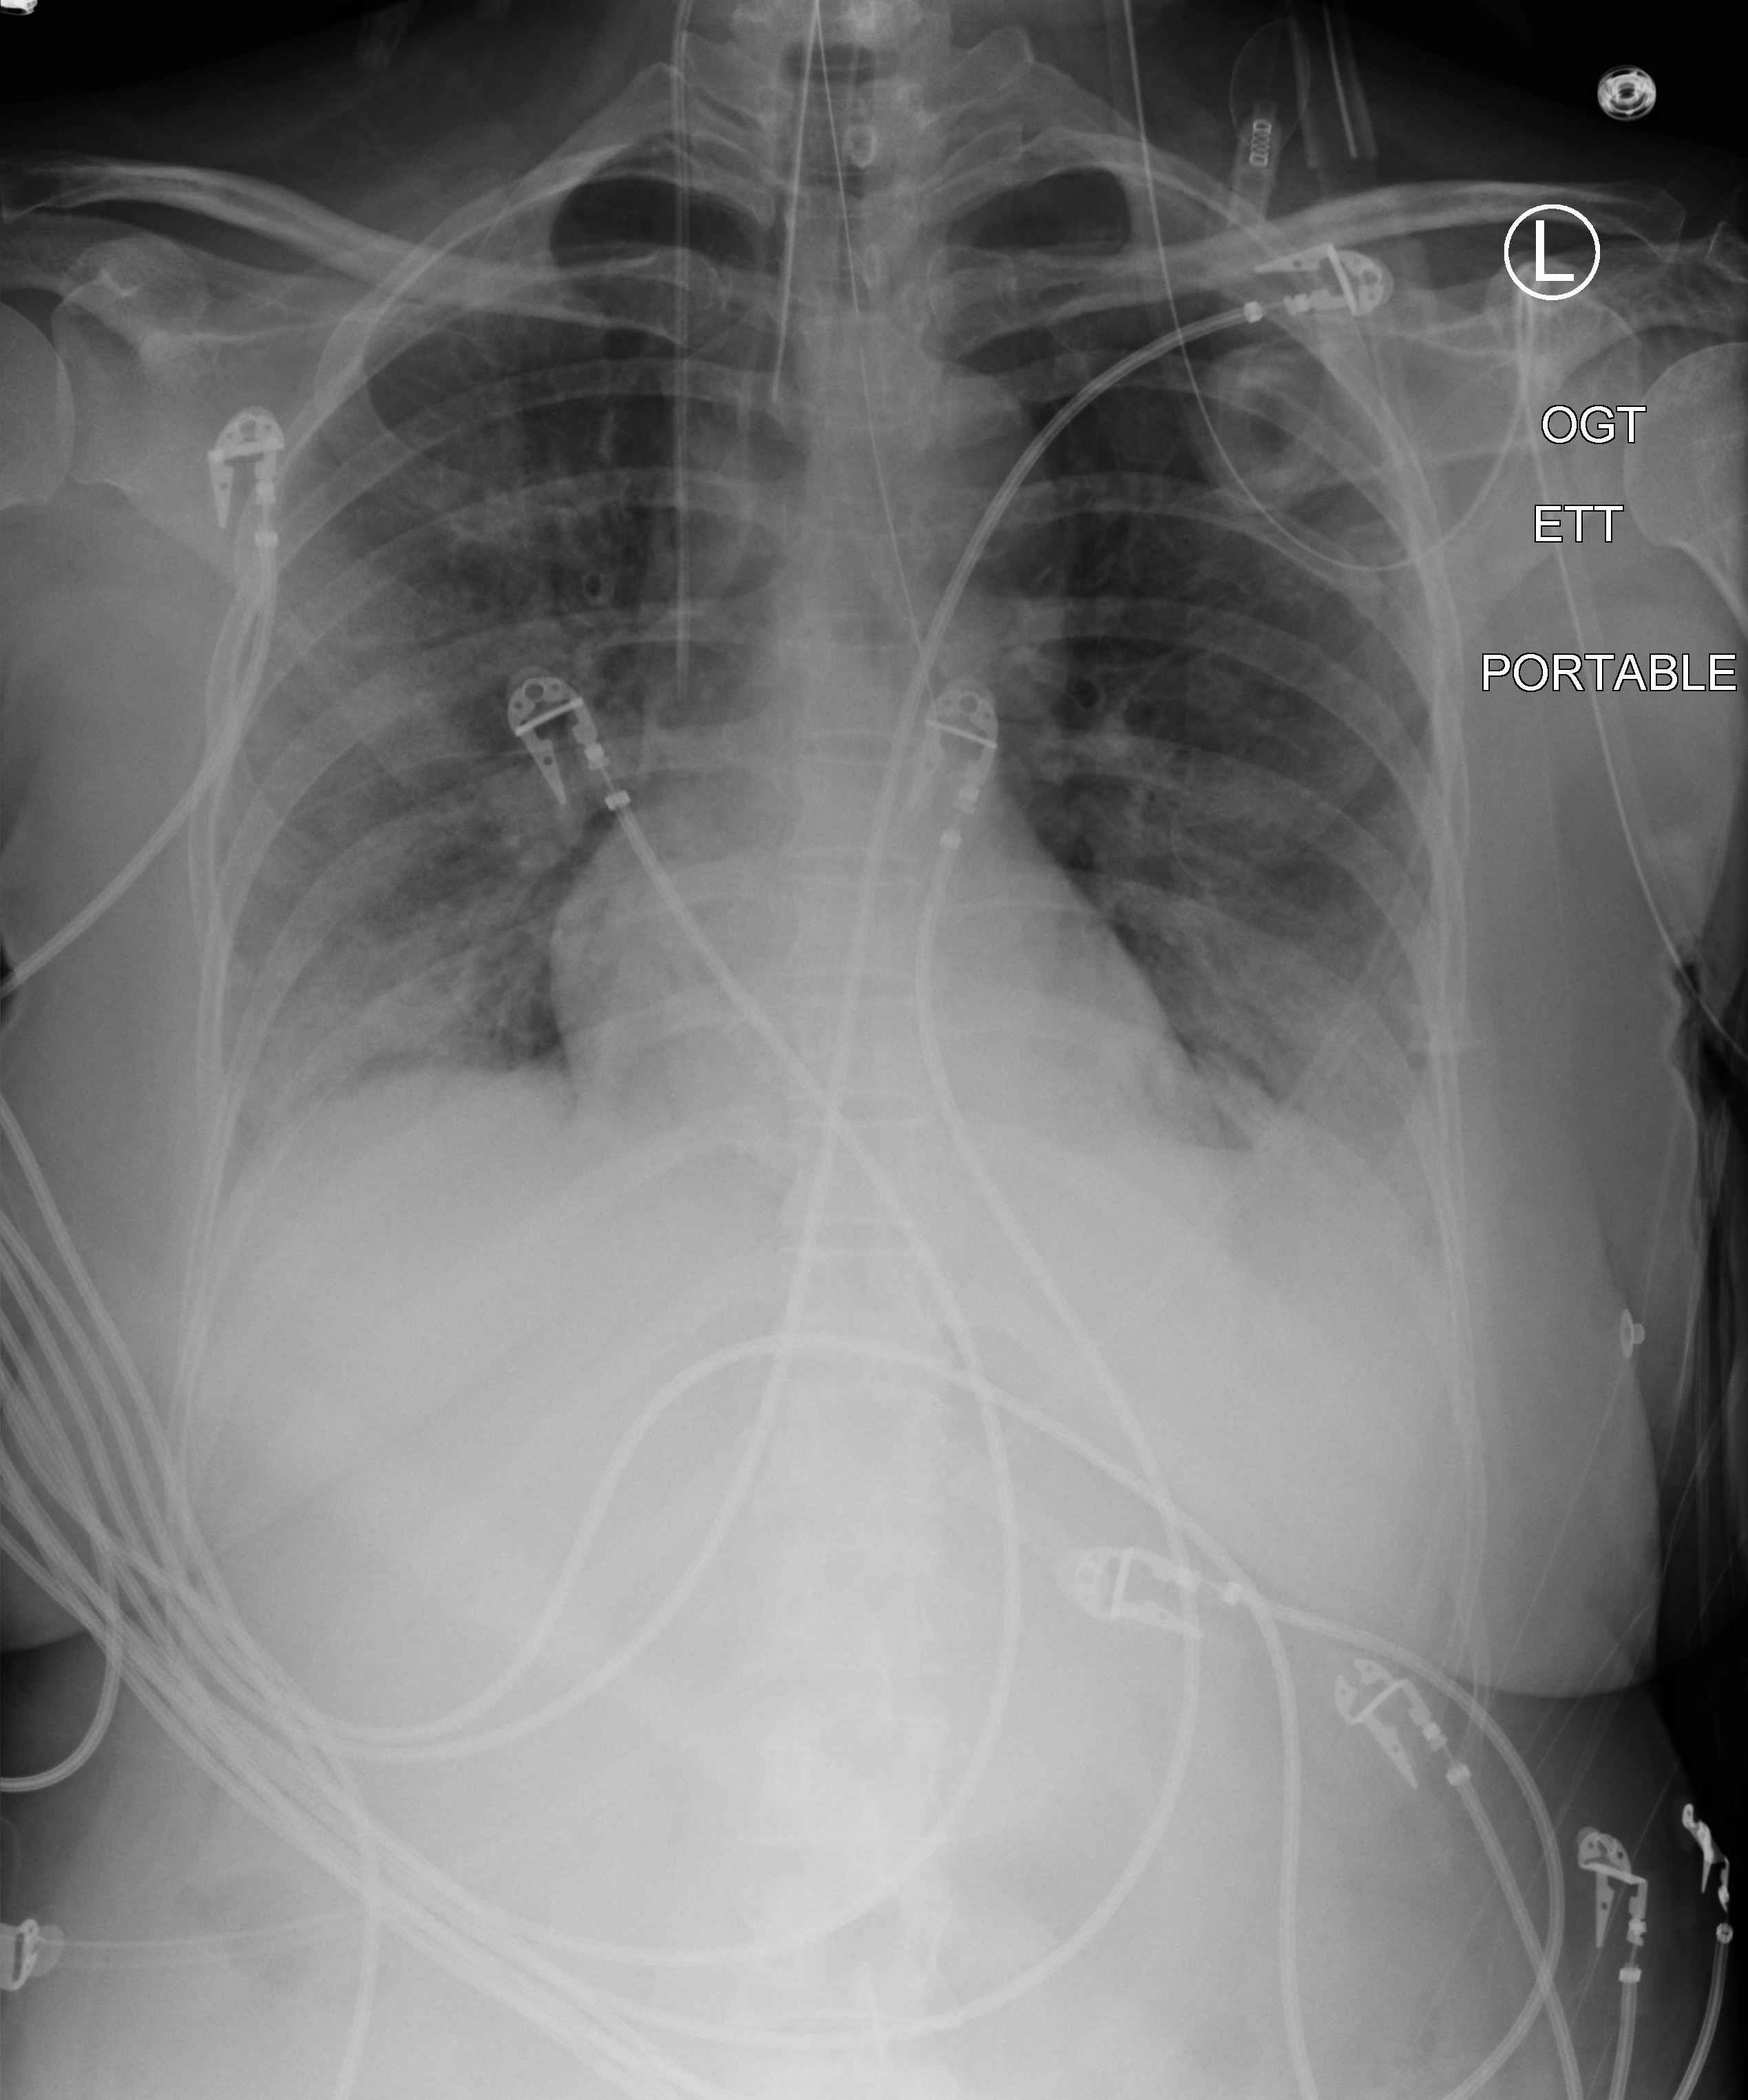
Chest X-ray (portable), anteroposterior (AP) projection. Female patient hospitalised with COVID-19, age 18–59 years.
From the hospital-stay record, not from the radiograph (when in the stay this image was taken is not recorded): admitted to intensive care during this hospital stay: yes; smoking status (admission record): never.